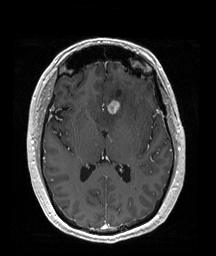
Brain MRI from a brain-tumour surgery series, one axial slice. Slice 94 of 192 in the series (ordered by position). T1-weighted post-contrast. 1 mm slice thickness. 216 × 256 image matrix, field of view 211 × 250 mm. From the clinical record (not read from this slice): histopathology: Oligodendroglioma; WHO grade: 2; IDH mutation: yes; tumour location: Left Frontal (septal).
Outlined on this slice (manually delineated by an expert):
- tumour: bounding box [x1, y1, x2, y2] px = [107, 99, 132, 113]